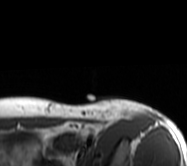
MRI of an extremity soft-tissue mass, one axial slice. Slice 50 of 62 in the series (ordered by position). MR volume resampled by the dataset authors to the PET/CT grid (not the native acquisition matrix). 3.27 mm slice thickness. 187 × 166 image matrix, field of view 183 × 162 mm. Female patient. Case-level facts recorded for this patient, not image findings: histological type: leiomyosarcoma; grade: high; site of the primary tumour: groin.
Annotated regions visible in this slice (expert contour drawn on MRI and transferred to this co-registered scan by the dataset authors):
- gross tumour volume including surrounding oedema: bounding box (x1, y1, x2, y2) in pixels: (87, 99, 161, 123)
- gross tumour volume (mass): (96, 112, 110, 118)